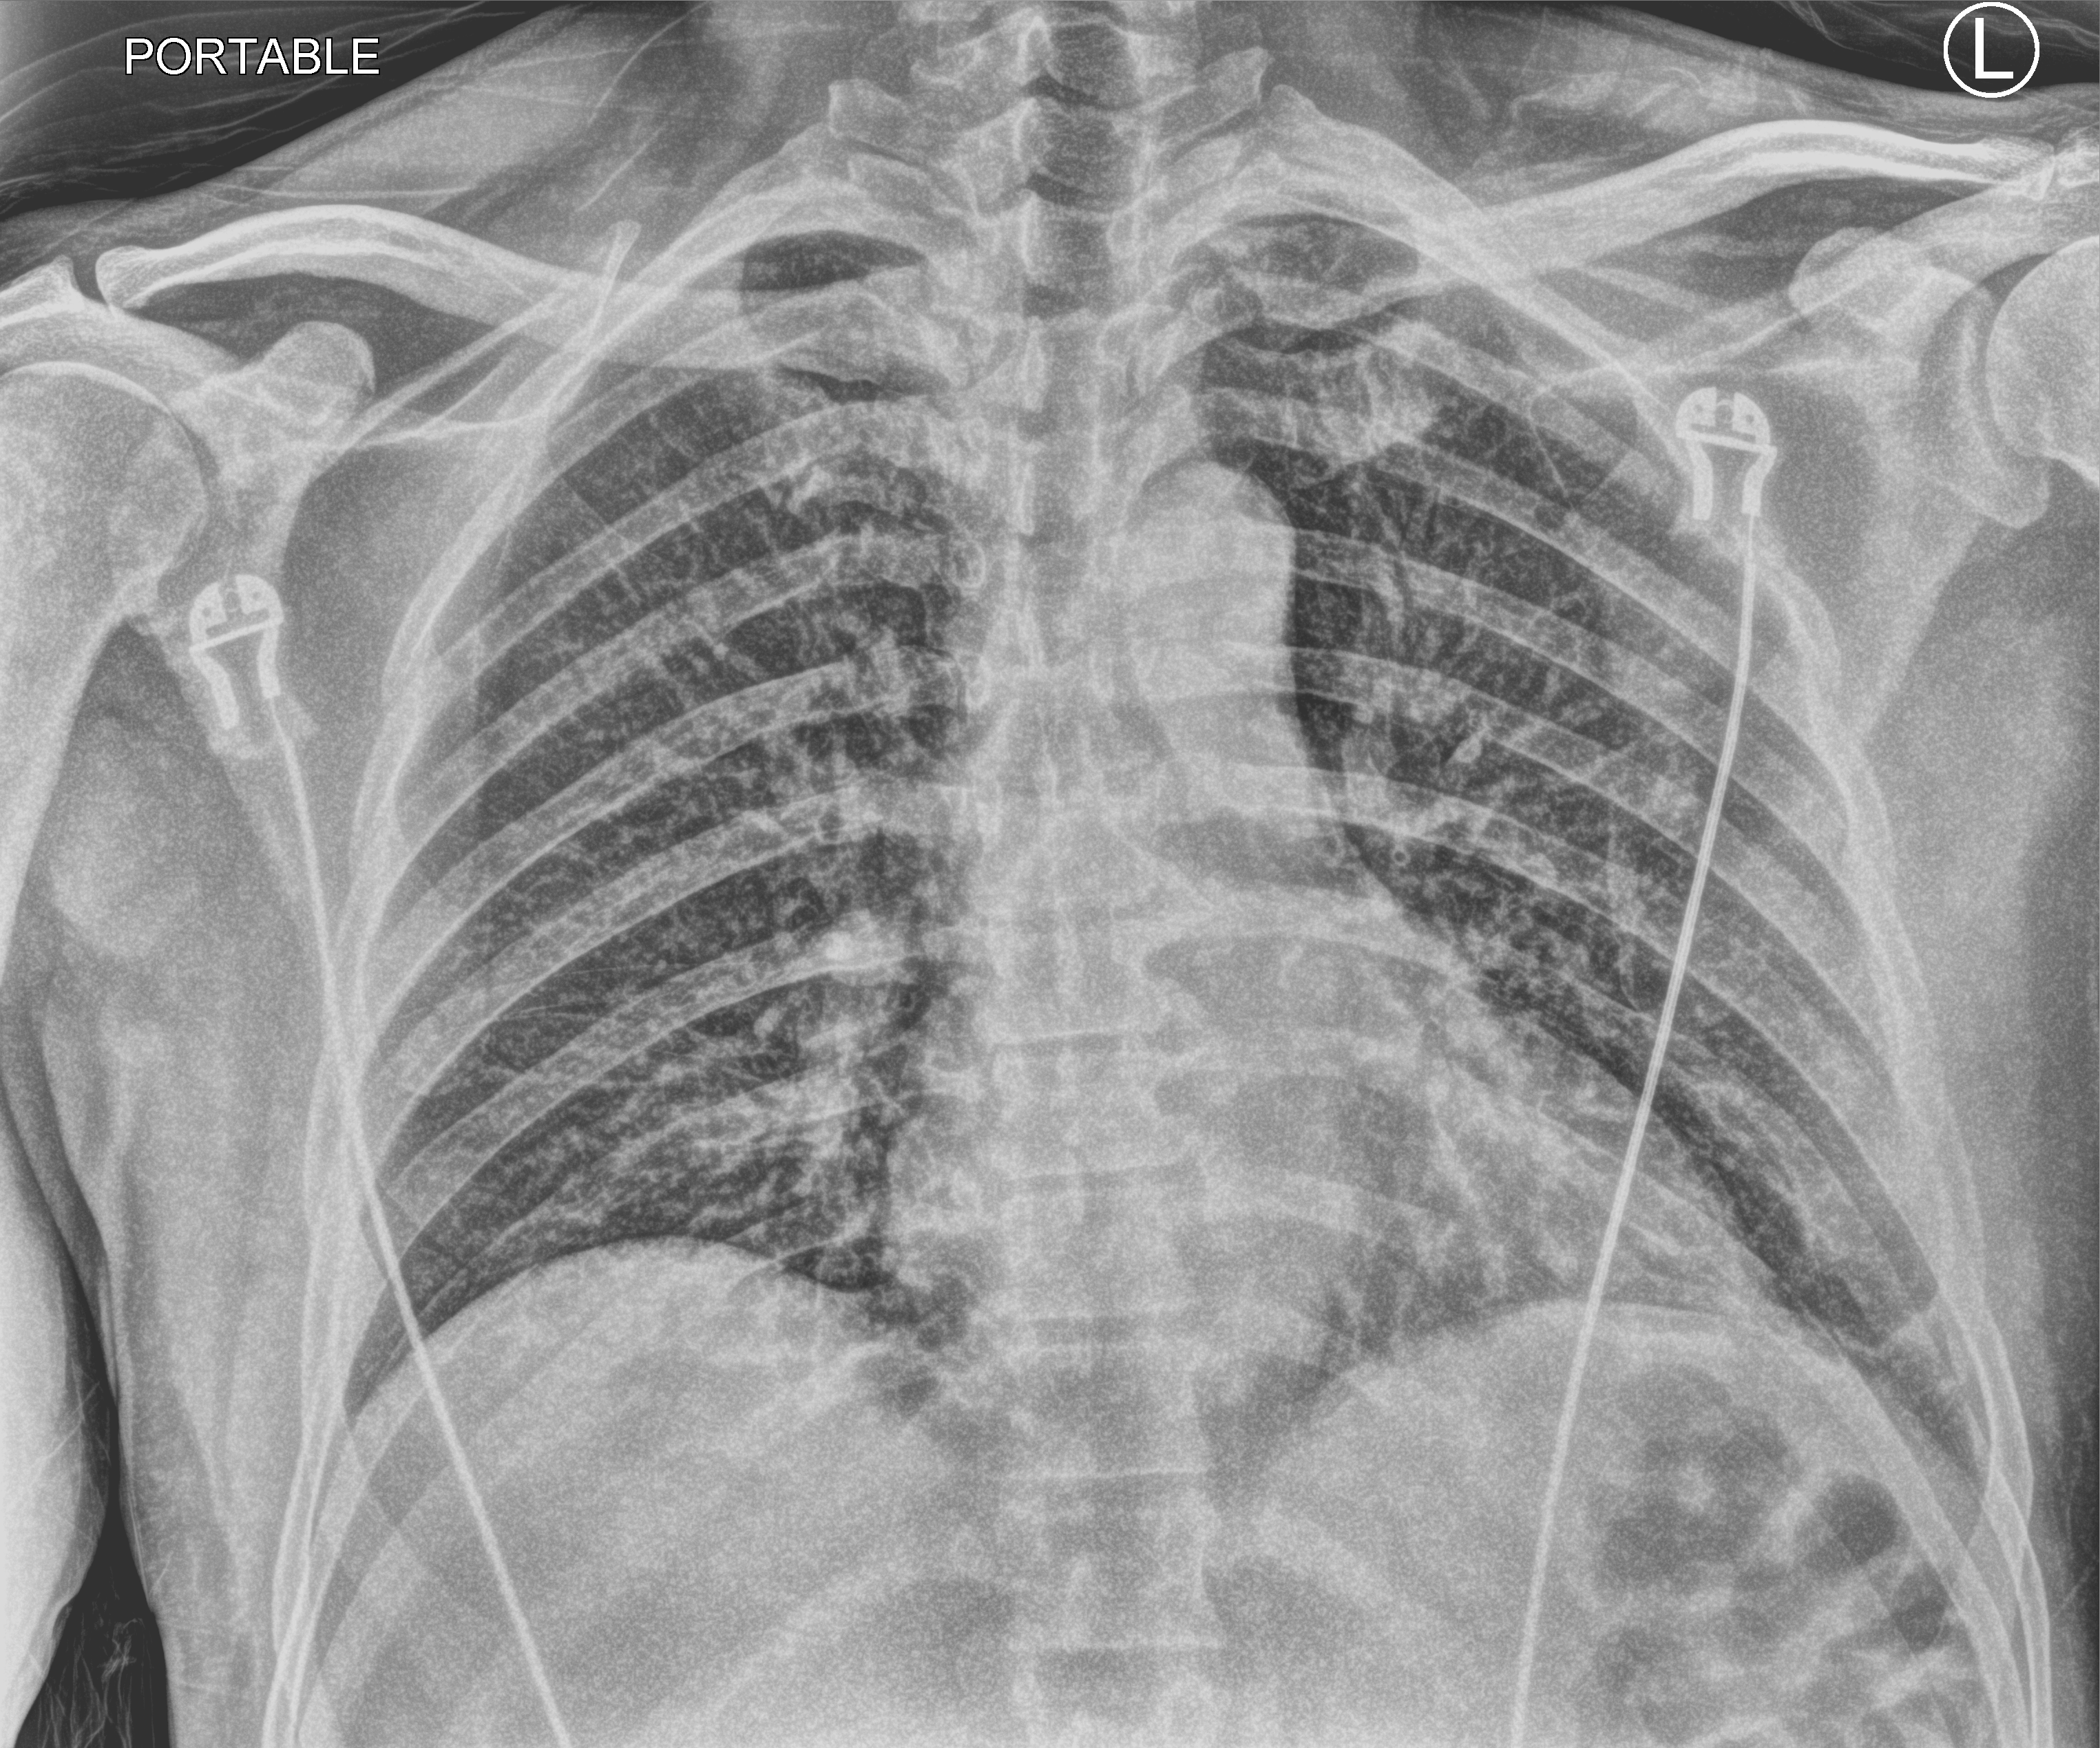
Portable chest radiograph; anteroposterior (AP) projection. Patient hospitalised with COVID-19; male, aged 18–59 years.
From the hospital-stay record, not from the radiograph (when in the stay this image was taken is not recorded):
- length of hospital stay: 1 day
- mechanically ventilated during this hospital stay: no
- admitted to intensive care during this hospital stay: no